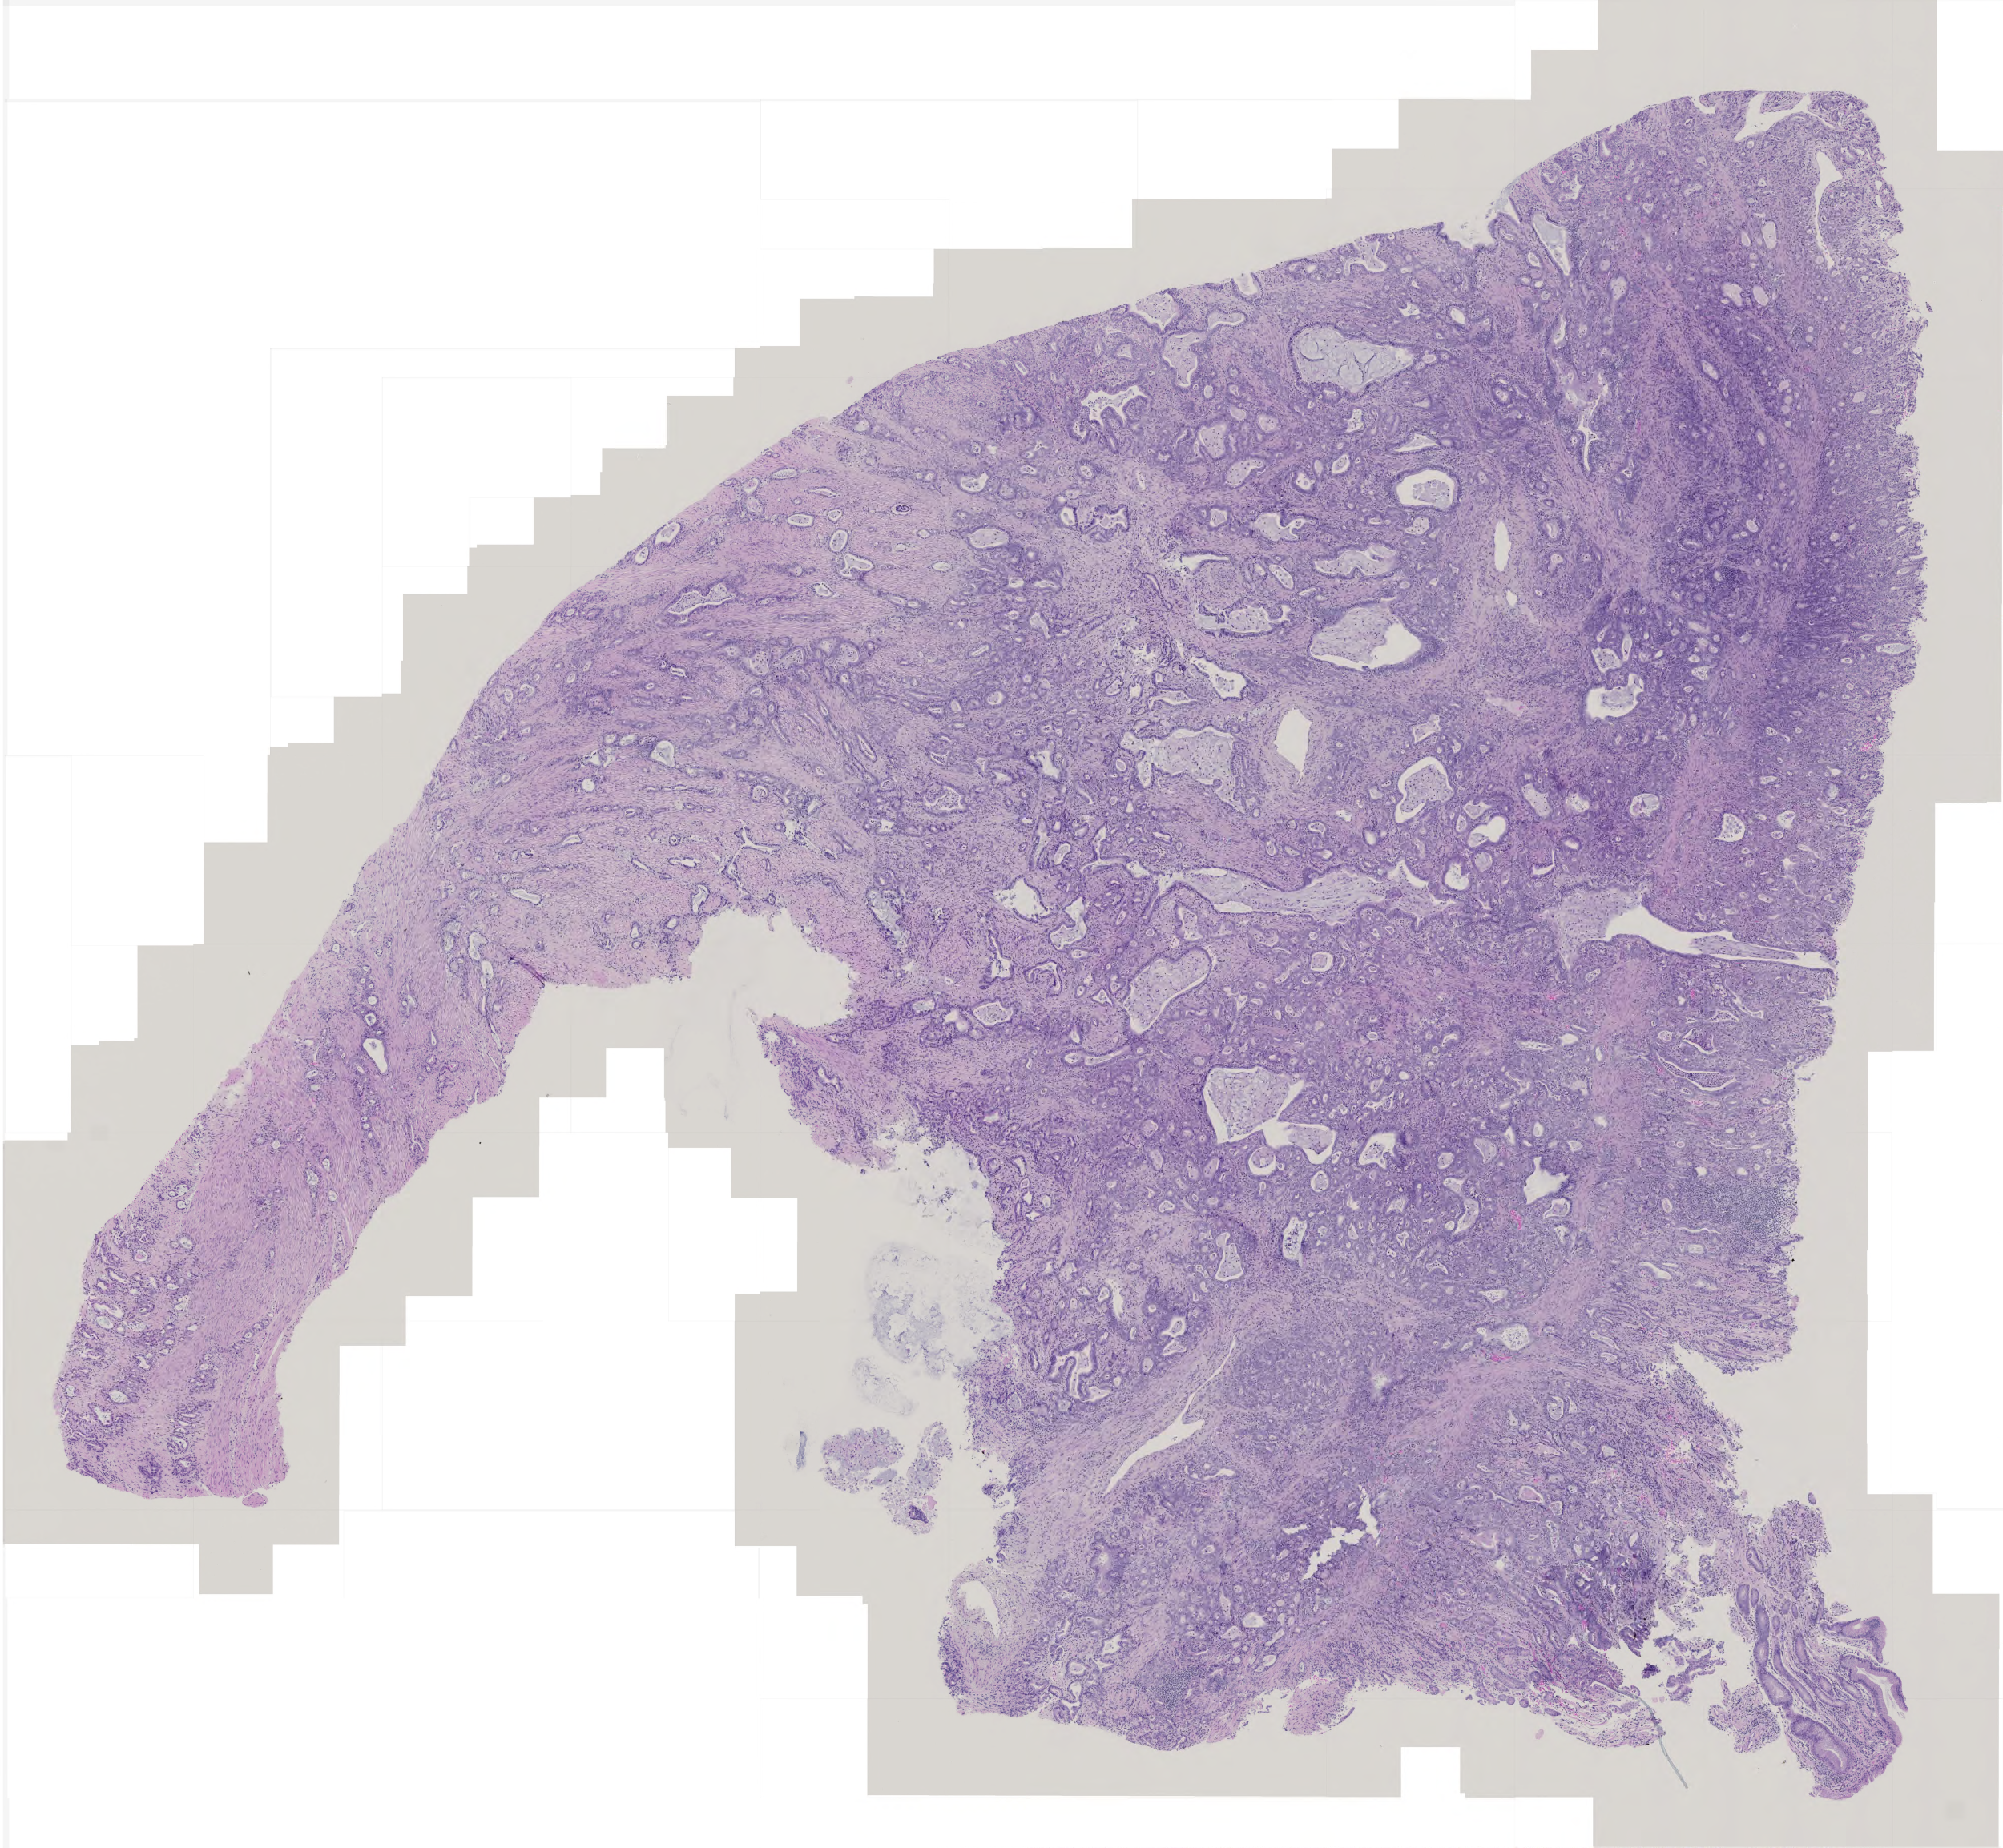
Digitized Hematoxylin and eosin (H&E) stained tissue section (whole slide), shown as a low-resolution overview of the whole scanned area (about 5.0 x 4.6 mm); formalin-fixed paraffin-embedded (FFPE) diagnostic section; stomach, primary tumour sample. Female, age 54 years at initial diagnosis. Histologic grade: G1 (well differentiated).
* TNM: T4 N0 M1
* diagnosis: Adenocarcinoma, intestinal type (body of stomach)
* lymph nodes positive (case pathology): 0 of 15 examined
* AJCC pathologic stage: IV